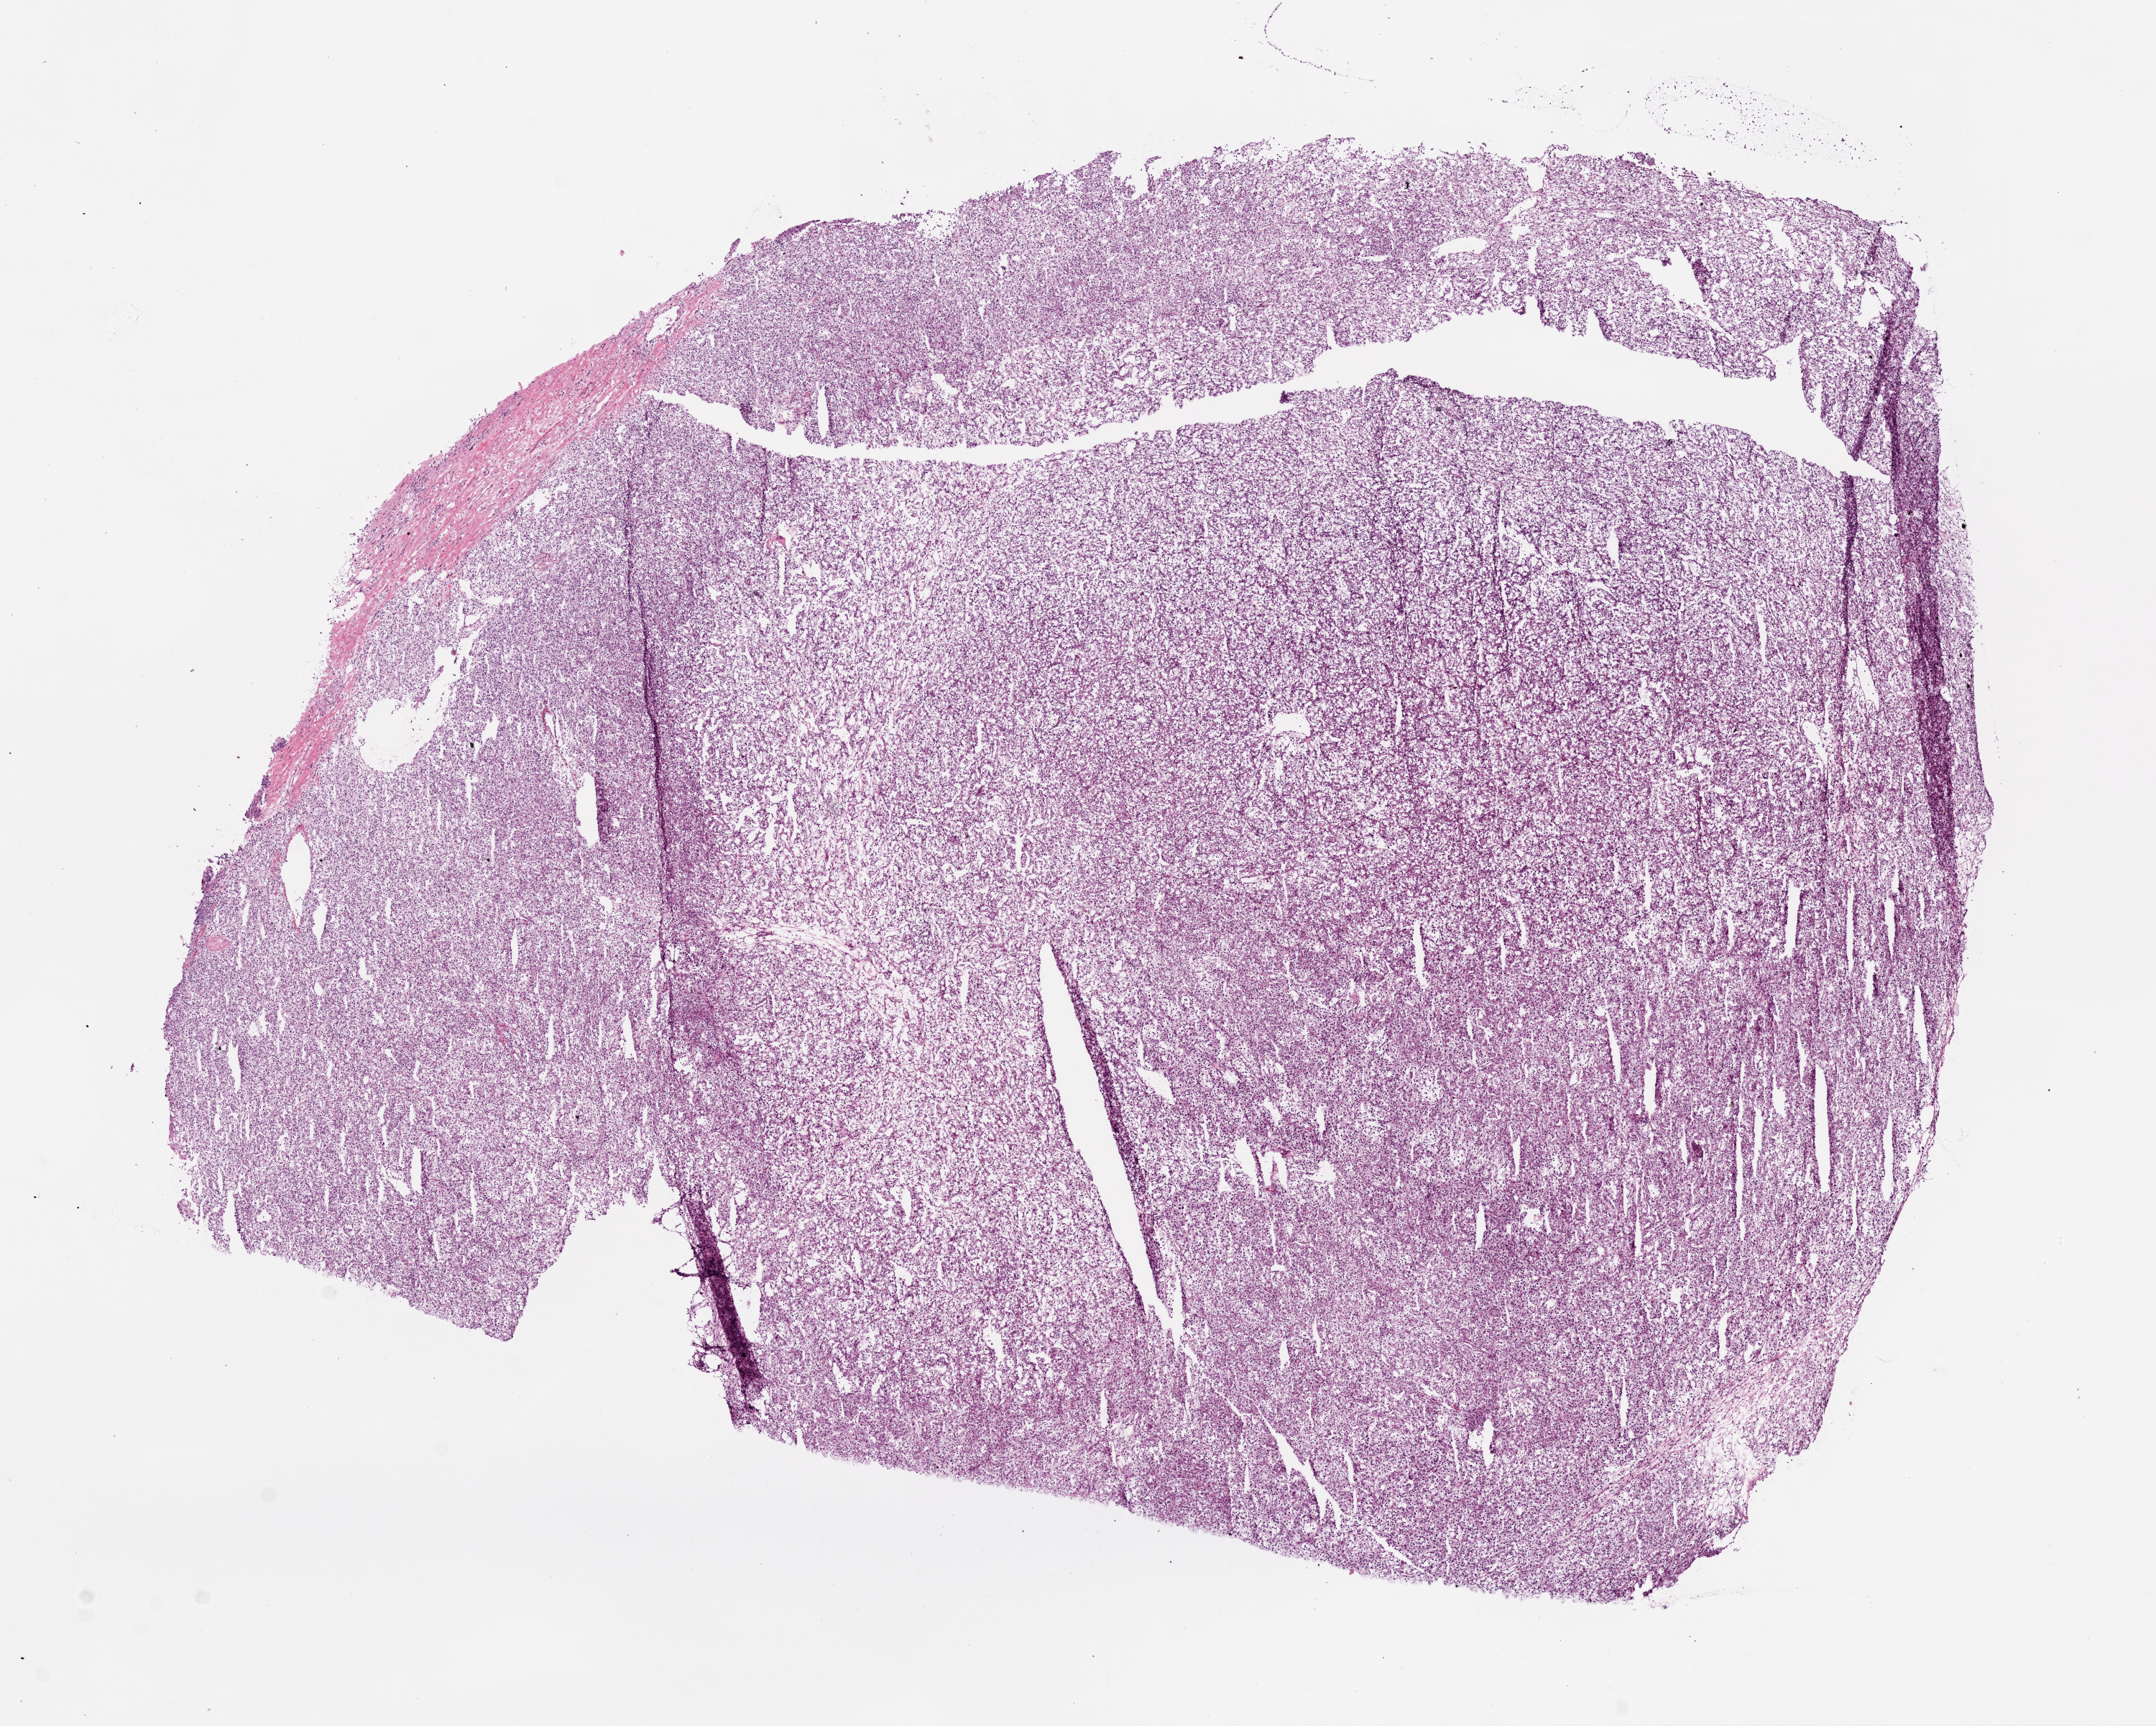
Digitized H&E-stained tissue section (whole slide) — low-resolution overview of the scanned area, about 12.0 x 9.6 mm; frozen section from the top of the tissue portion; primary tumour sample from the kidney. Male patient; age at initial diagnosis 53 years. Histologic grade: G2 (moderately differentiated). Slide review estimates, as recorded: tumour cells 92%, tumour nuclei 85%, normal cells 0%, stromal cells 8%, necrosis 0%.
AJCC pathologic stage: I (6th edition). Diagnosis: Clear cell adenocarcinoma, NOS.